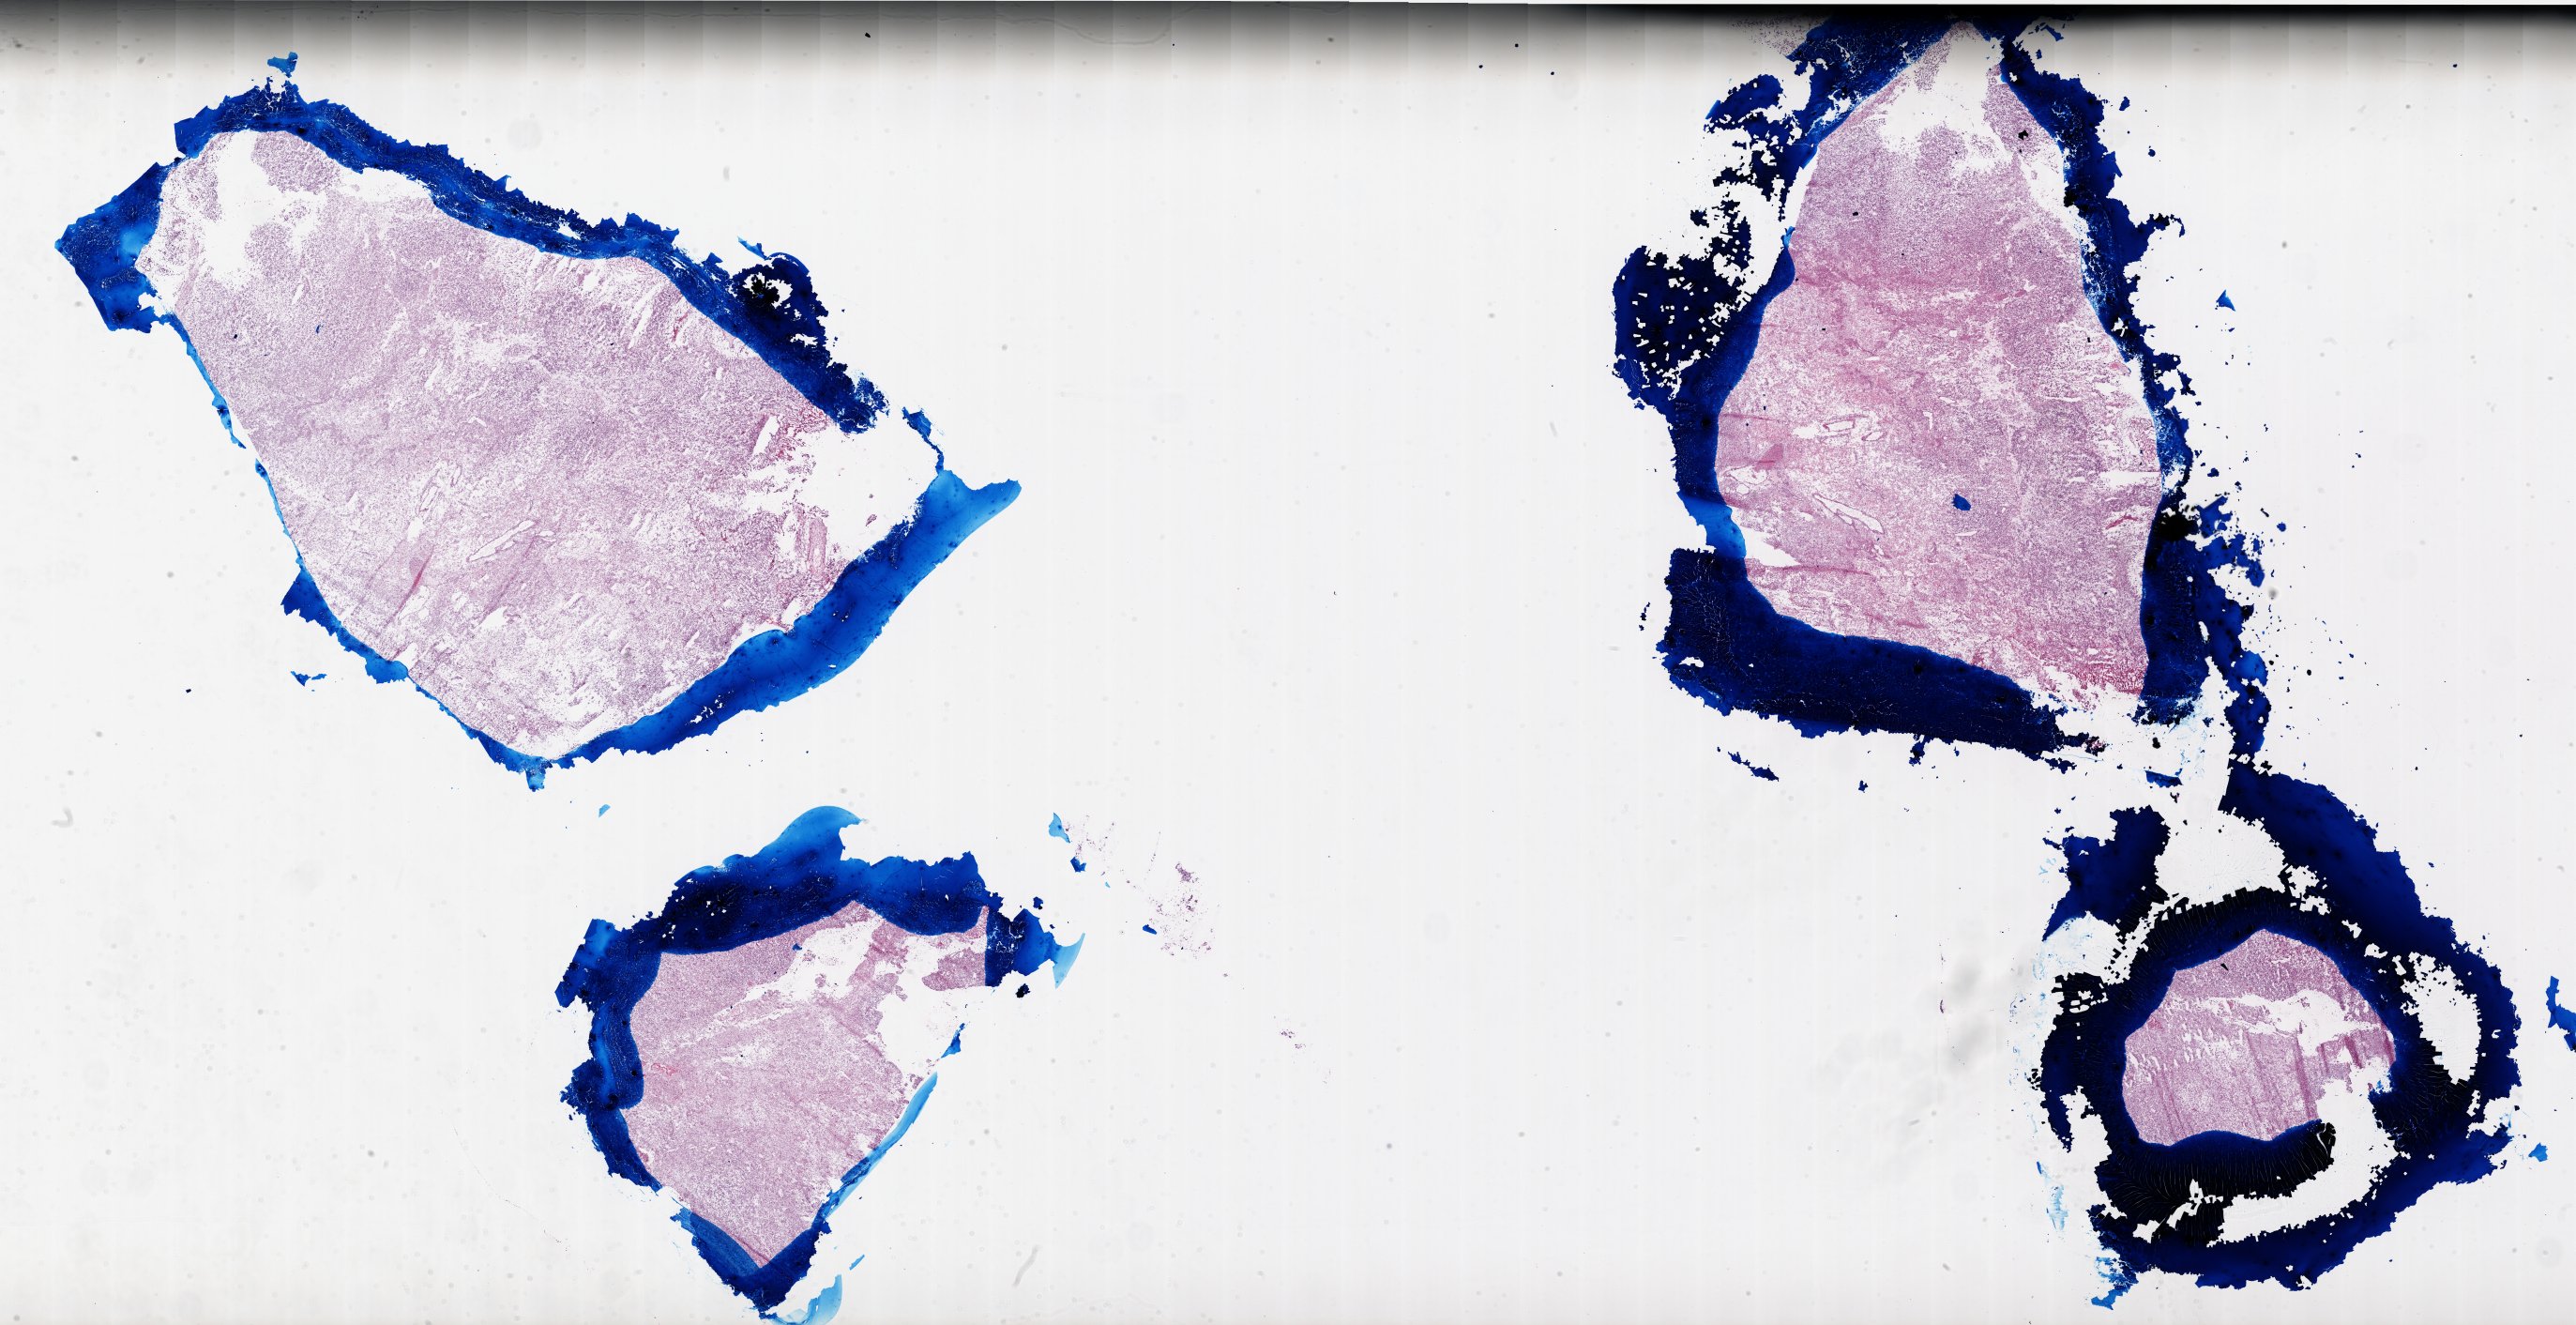
Whole-slide histology image, Hematoxylin and eosin (H&E) stained — shown as a low-resolution overview of the whole scanned area (about 44.0 x 22.6 mm, acquisition: 20x scan). Frozen section from the top of the tissue portion. Sample: primary tumour, brain. Male patient; age at initial diagnosis 49 years. Slide review estimates, as recorded: tumour cells 85%, tumour nuclei 100%, normal cells 0%, stromal cells 0%, necrosis 15%.
- diagnosis: Glioblastoma